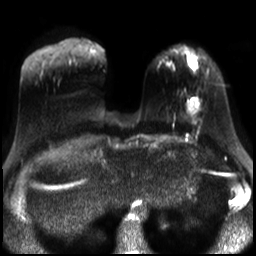
Breast MRI, one axial slice. Slice 7 of 30 in the series (ordered by position). Diffusion-weighted series; image 2 of 4 stored at this slice position (different b-values; order by instance number). 3 T. 4 mm slice thickness. 256 × 256 image matrix, field of view 320 × 320 mm. Female patient.
Outlined on this slice (expert manual segmentation):
- tumour on diffusion-weighted imaging: bounding box <187,100,200,113> (left, top, right, bottom; pixels)